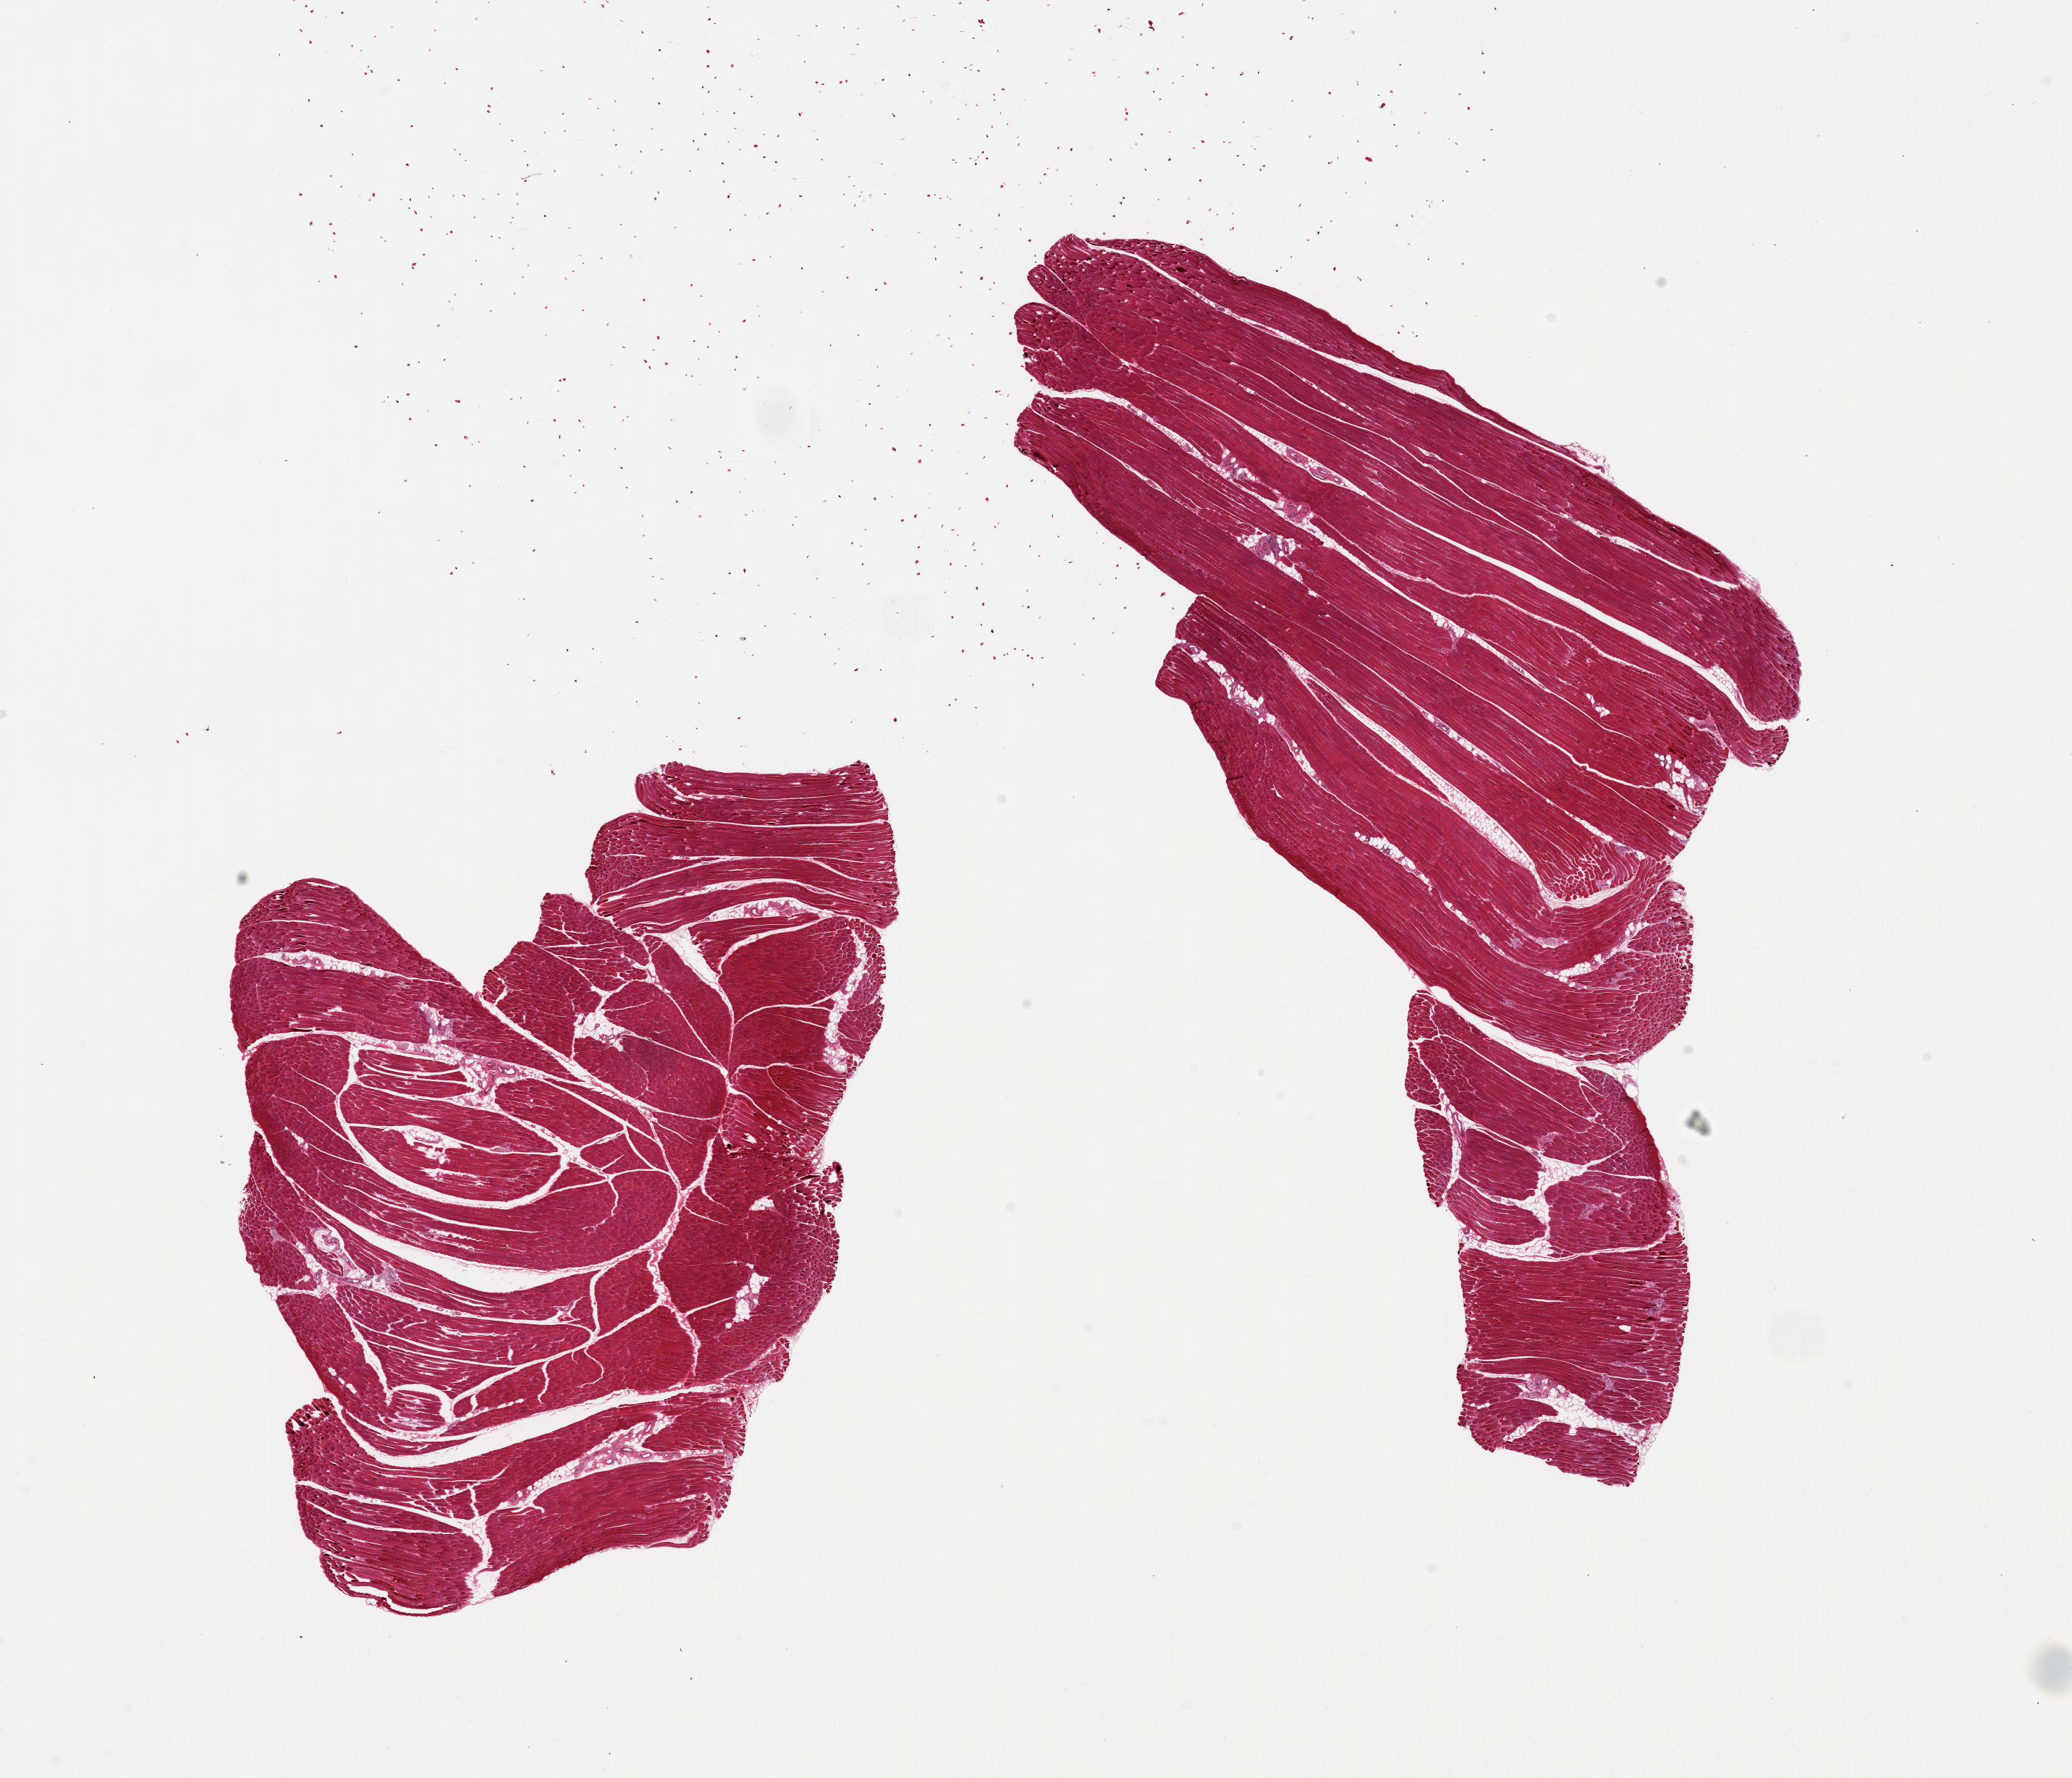
Haematoxylin and eosin whole-slide image, brightfield, whole scanned area (about 22.6 x 19.4 mm, slide scanned at 20x) shown as a low-resolution overview; PAXgene-fixed paraffin-embedded (PFPE) section; target tissue: skeletal muscle; tissue donor sample. Female donor.
Reviewer comment on this tissue sample: 2 pieces, 10x7 & 11x10mm; less than 2% interstitial fat, good specimens.